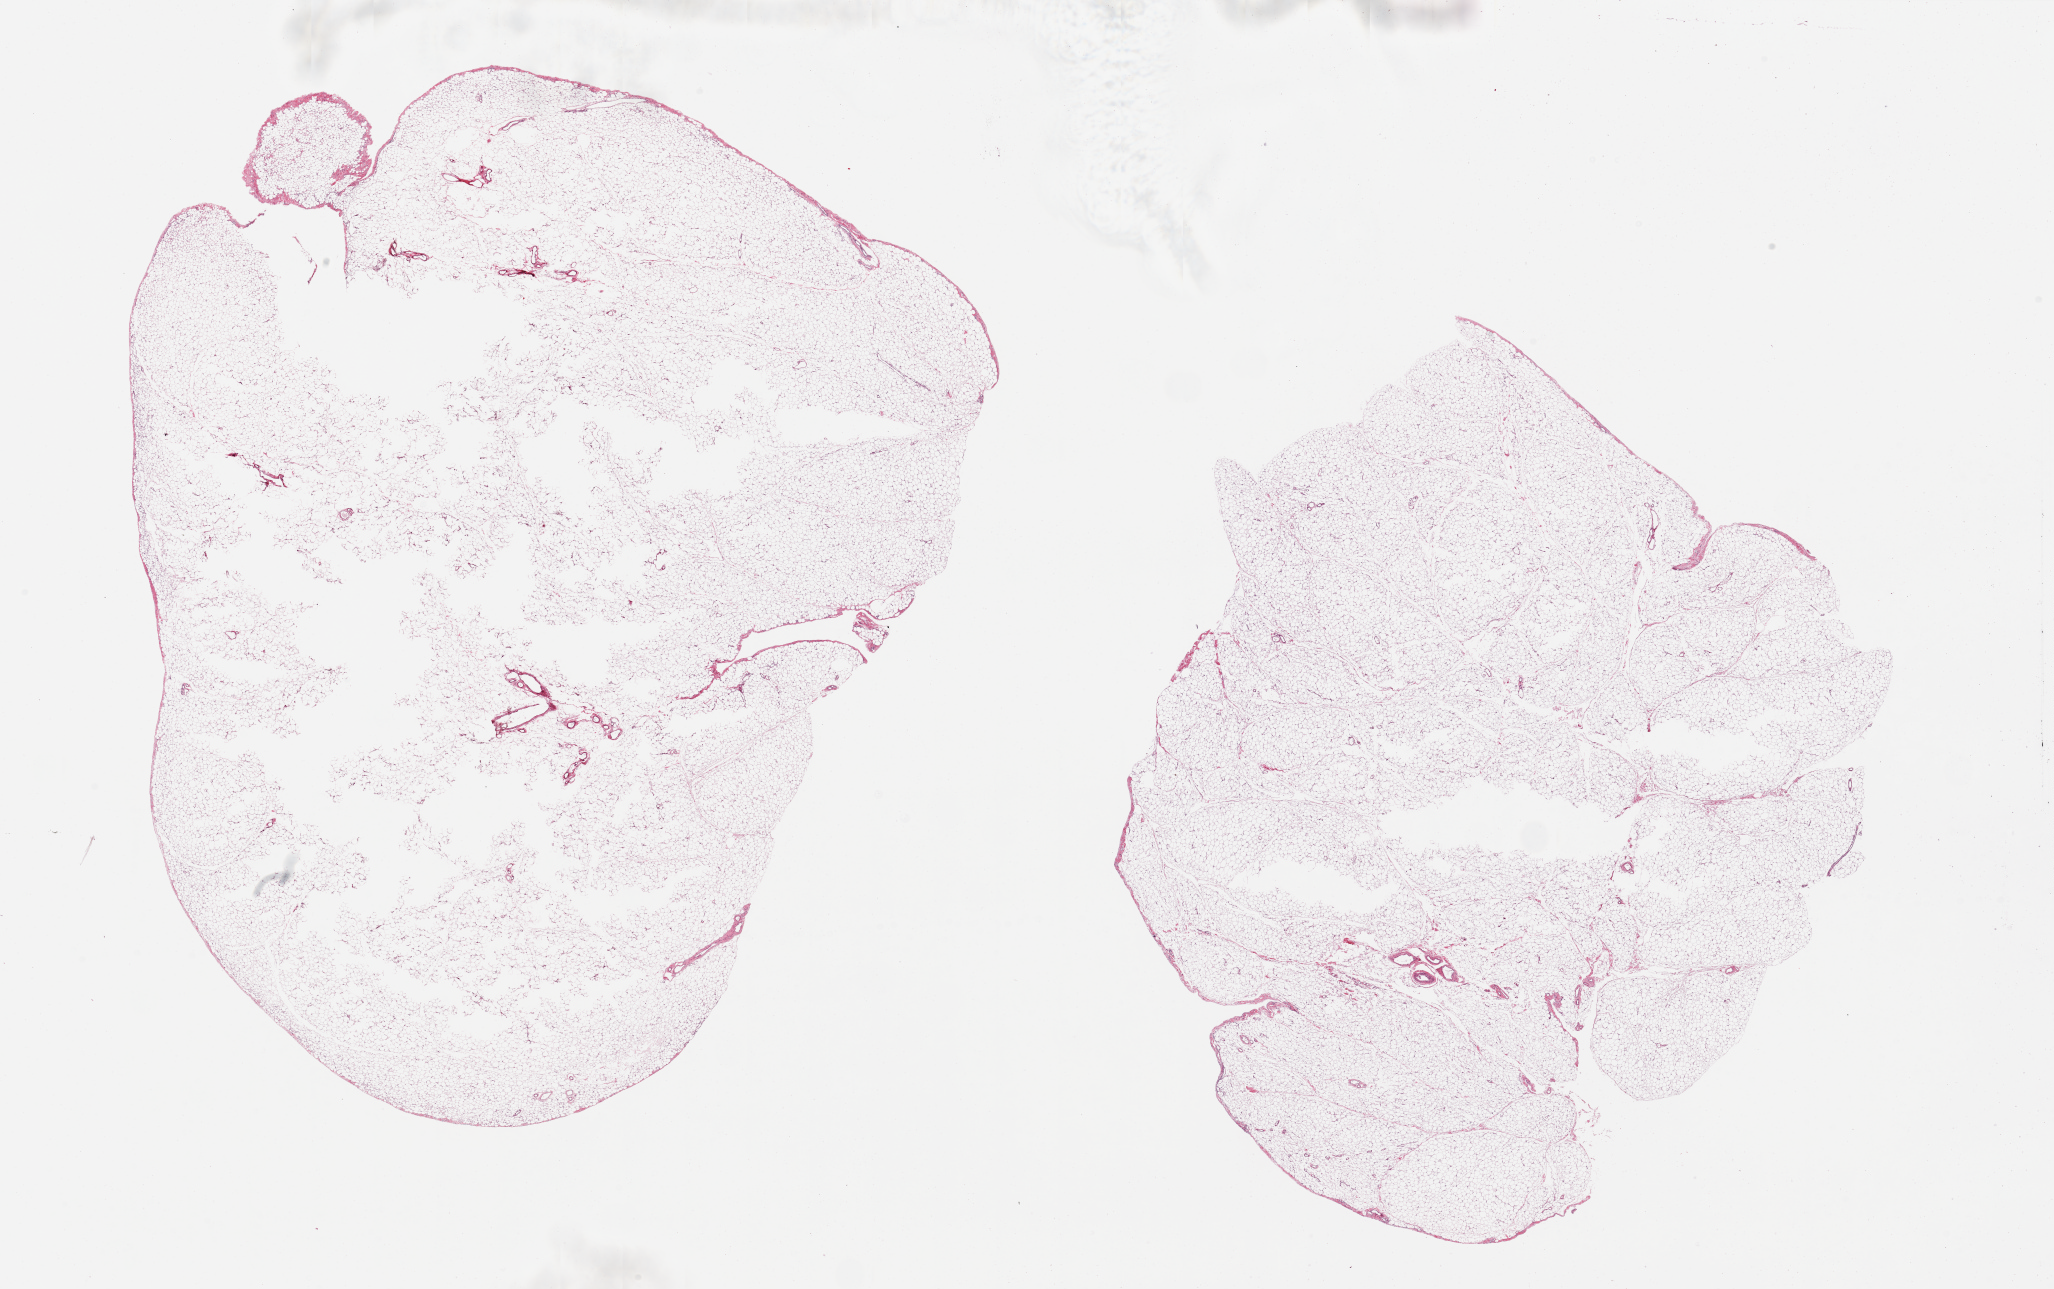
Whole-slide image, haematoxylin and eosin stain, brightfield, a low-resolution overview of the entire scanned area, about 32.5 x 20.4 mm. PAXgene-fixed paraffin-embedded (PFPE) section. Sampled site (target tissue): omentum. Tissue donor sample. Donor: female.
Reviewer comment on this tissue sample: 2 pieces, central defects in both (? poor fixation).